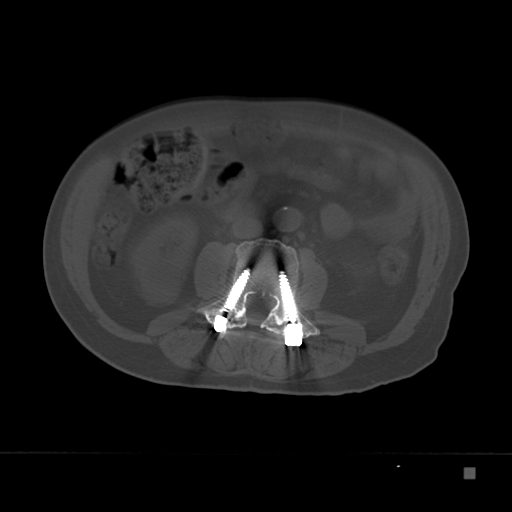
CT including the spine, one axial slice. Reconstruction kernel Br40s. 120 kVp. Bone window (W 1800 / L 400 HU). 512 × 512 image matrix. Male patient, age 72 years. From the clinical record (not read from this slice): primary cancer: skeletal.
Structures marked on this image (semi-automatic segmentation, software-assisted and operator-edited):
- L3 vertebra: box from (x=196, y=238) to (x=322, y=338) px